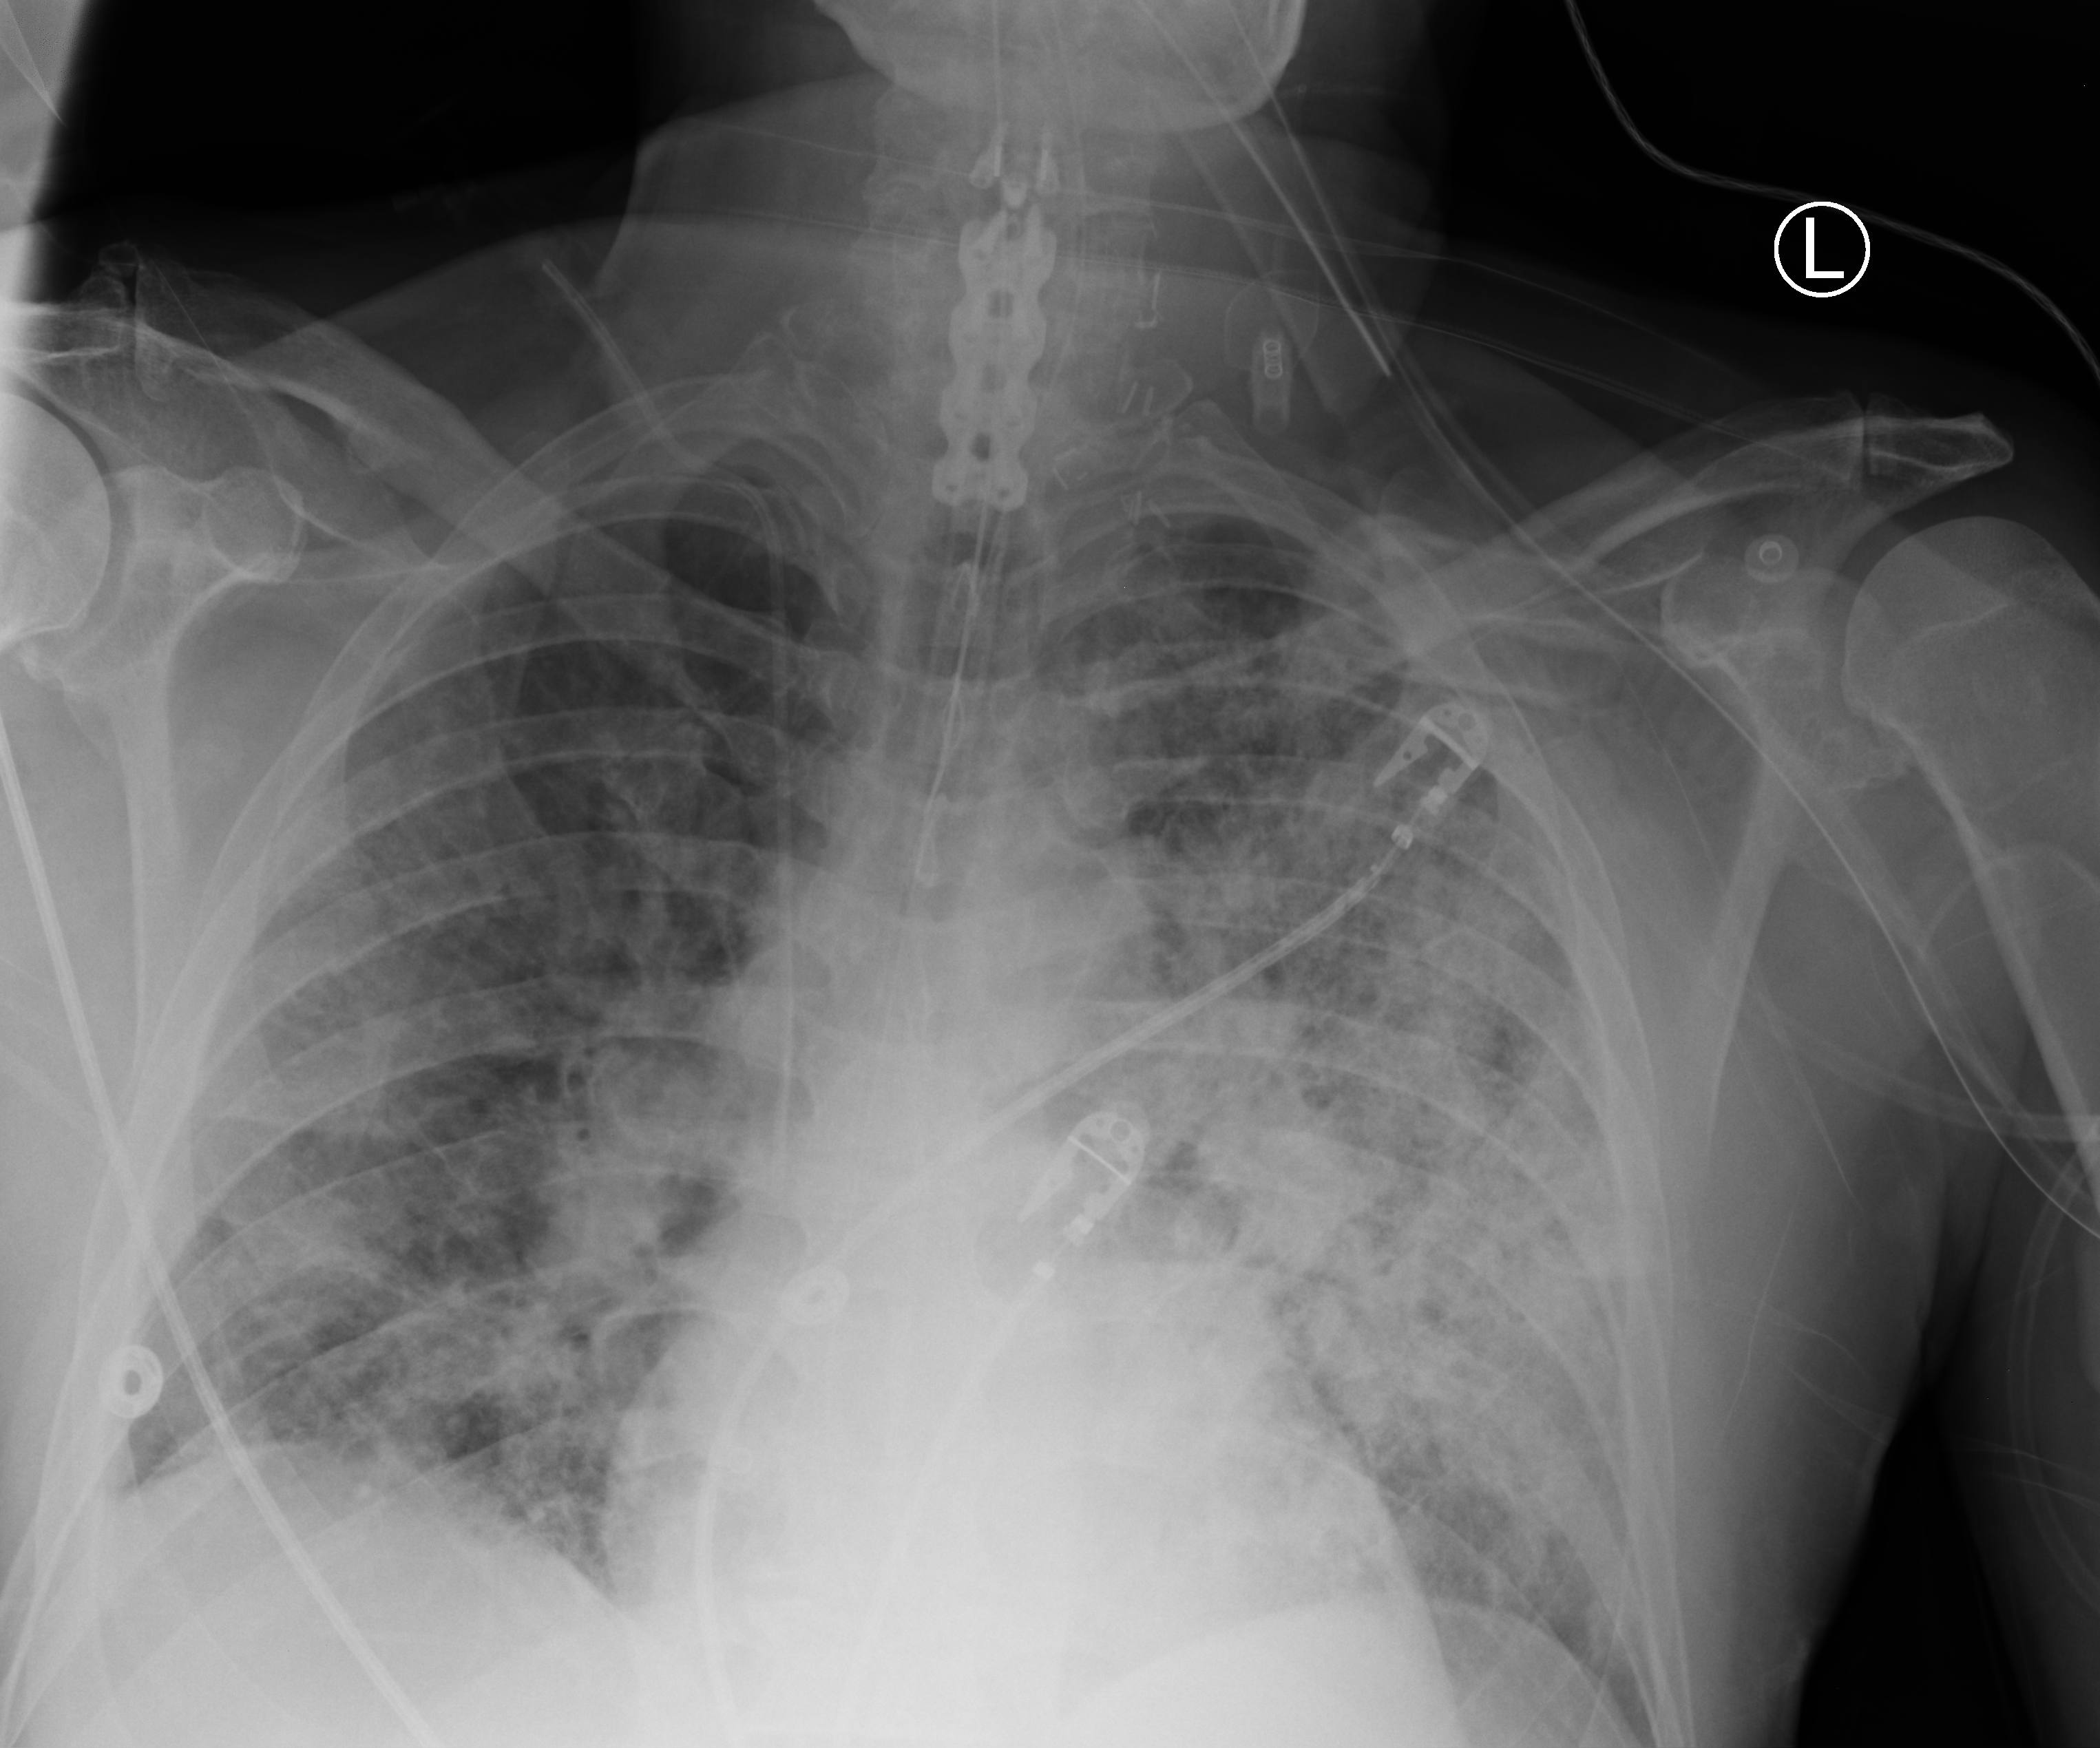
Bedside chest radiograph (computed radiography). Patient hospitalised with COVID-19; male, aged 60–74 years.
Admission-level facts for this patient (not findings on this image; timing relative to this image not recorded): mechanically ventilated during this hospital stay: yes; admitted to intensive care during this hospital stay: yes.